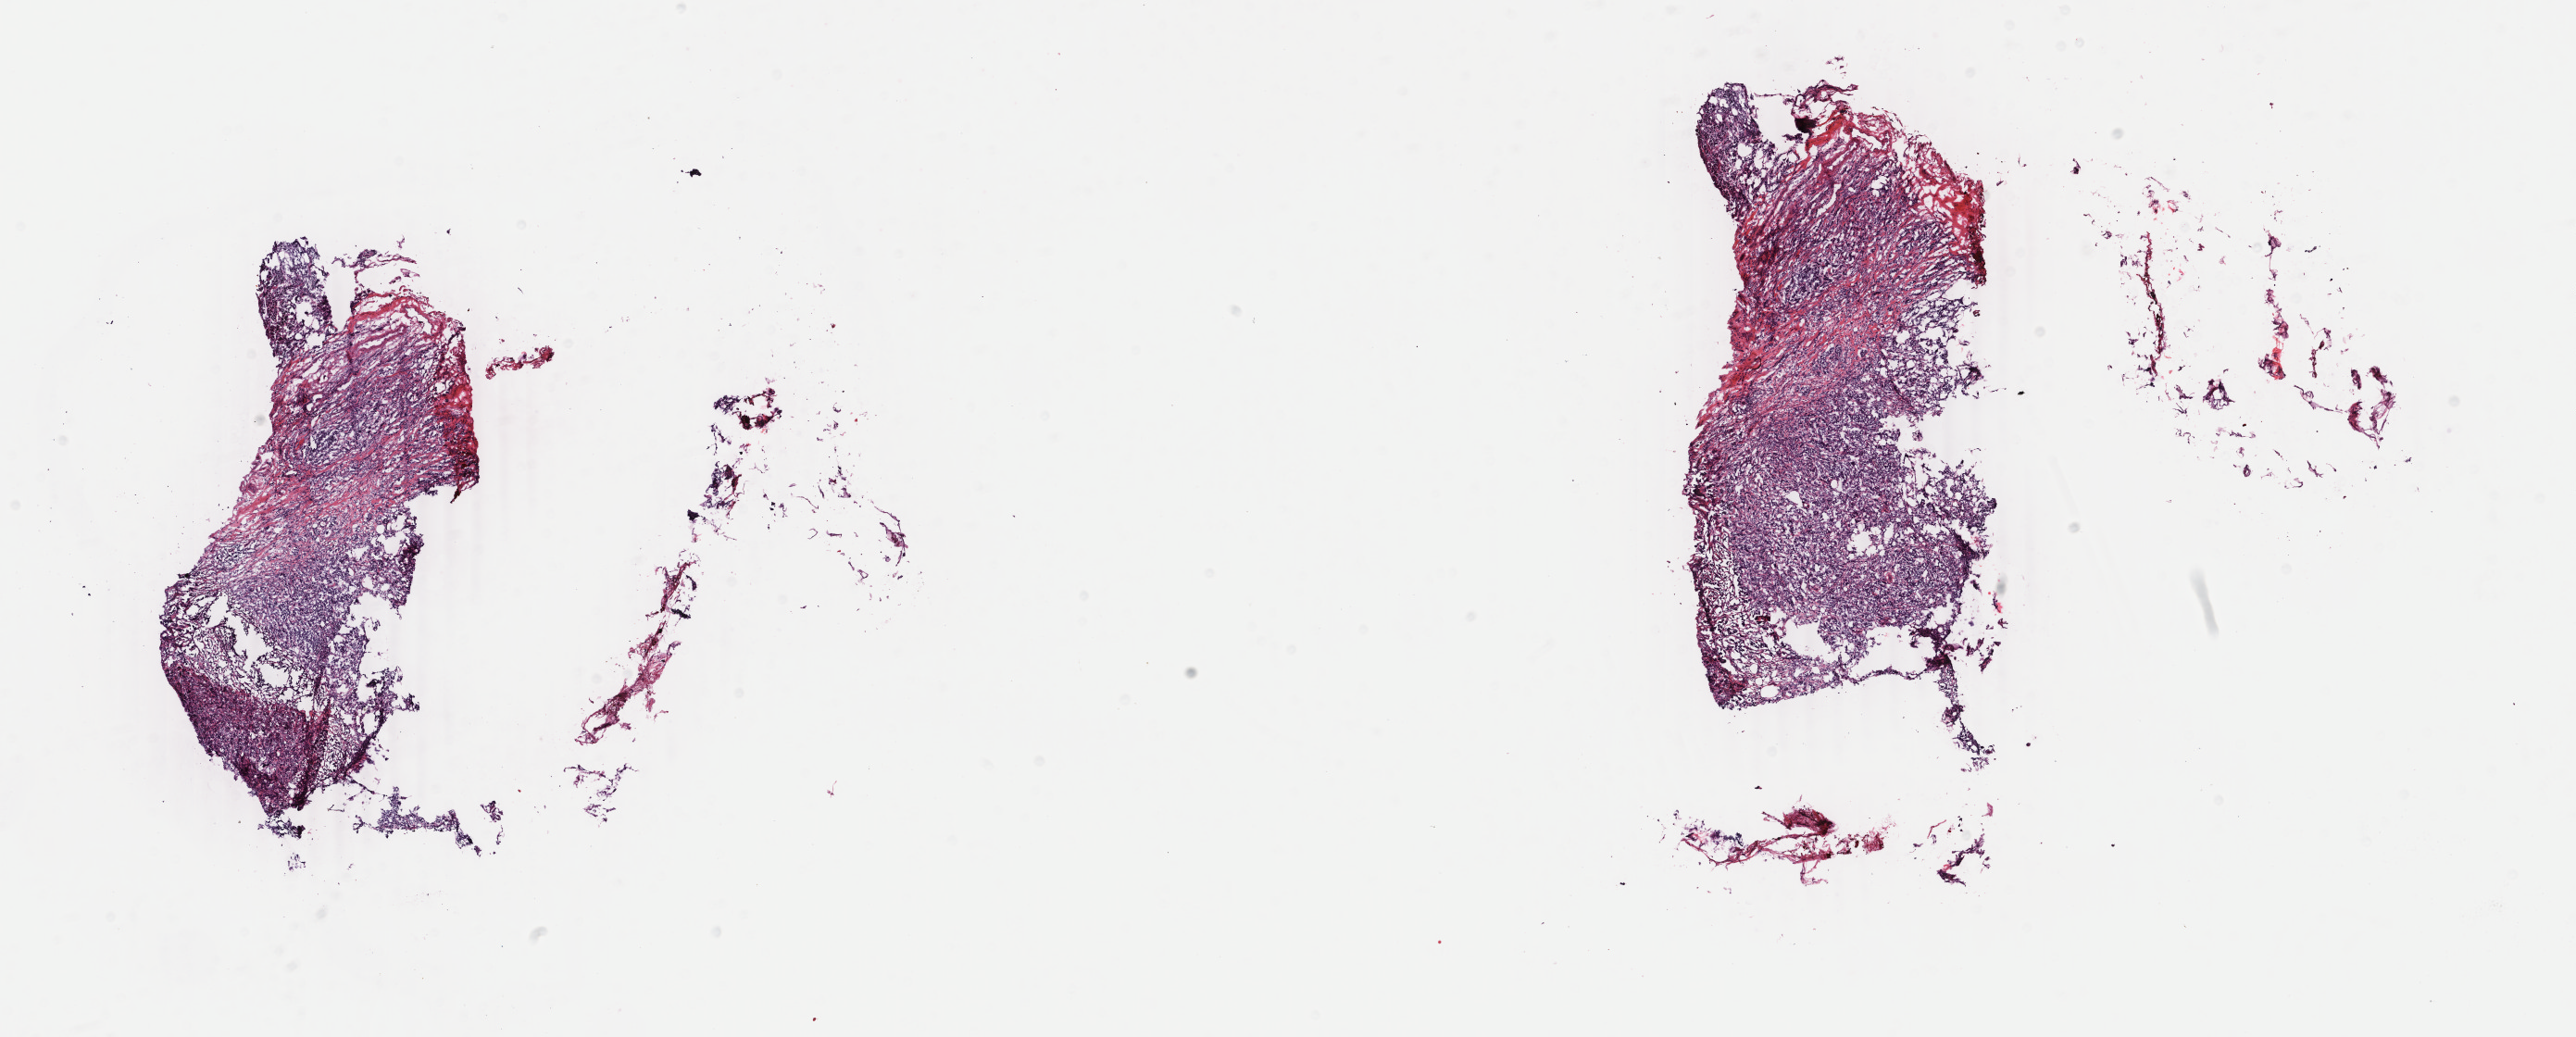
Whole-slide histology image, H&E-stained — a low-resolution overview of the entire scanned area, about 22.1 x 8.9 mm (from a 40x scan). Frozen section from the bottom of the tissue portion. Breast, primary tumour sample. Patient: female, age at initial diagnosis 82 years. Composition of this section per pathologist review: tumour cells 80%, tumour nuclei 88%, normal cells 0%, stromal cells 20%, necrosis 0%. Infiltration values recorded for this section: lymphocyte infiltration 1%, monocyte infiltration 0%, neutrophil infiltration 0%.
AJCC pathologic stage: IV. Diagnosis: Infiltrating duct carcinoma, NOS. Laterality: right. TNM: T2 N2 M1. Lymph nodes positive (case pathology): 4 of 15 examined.